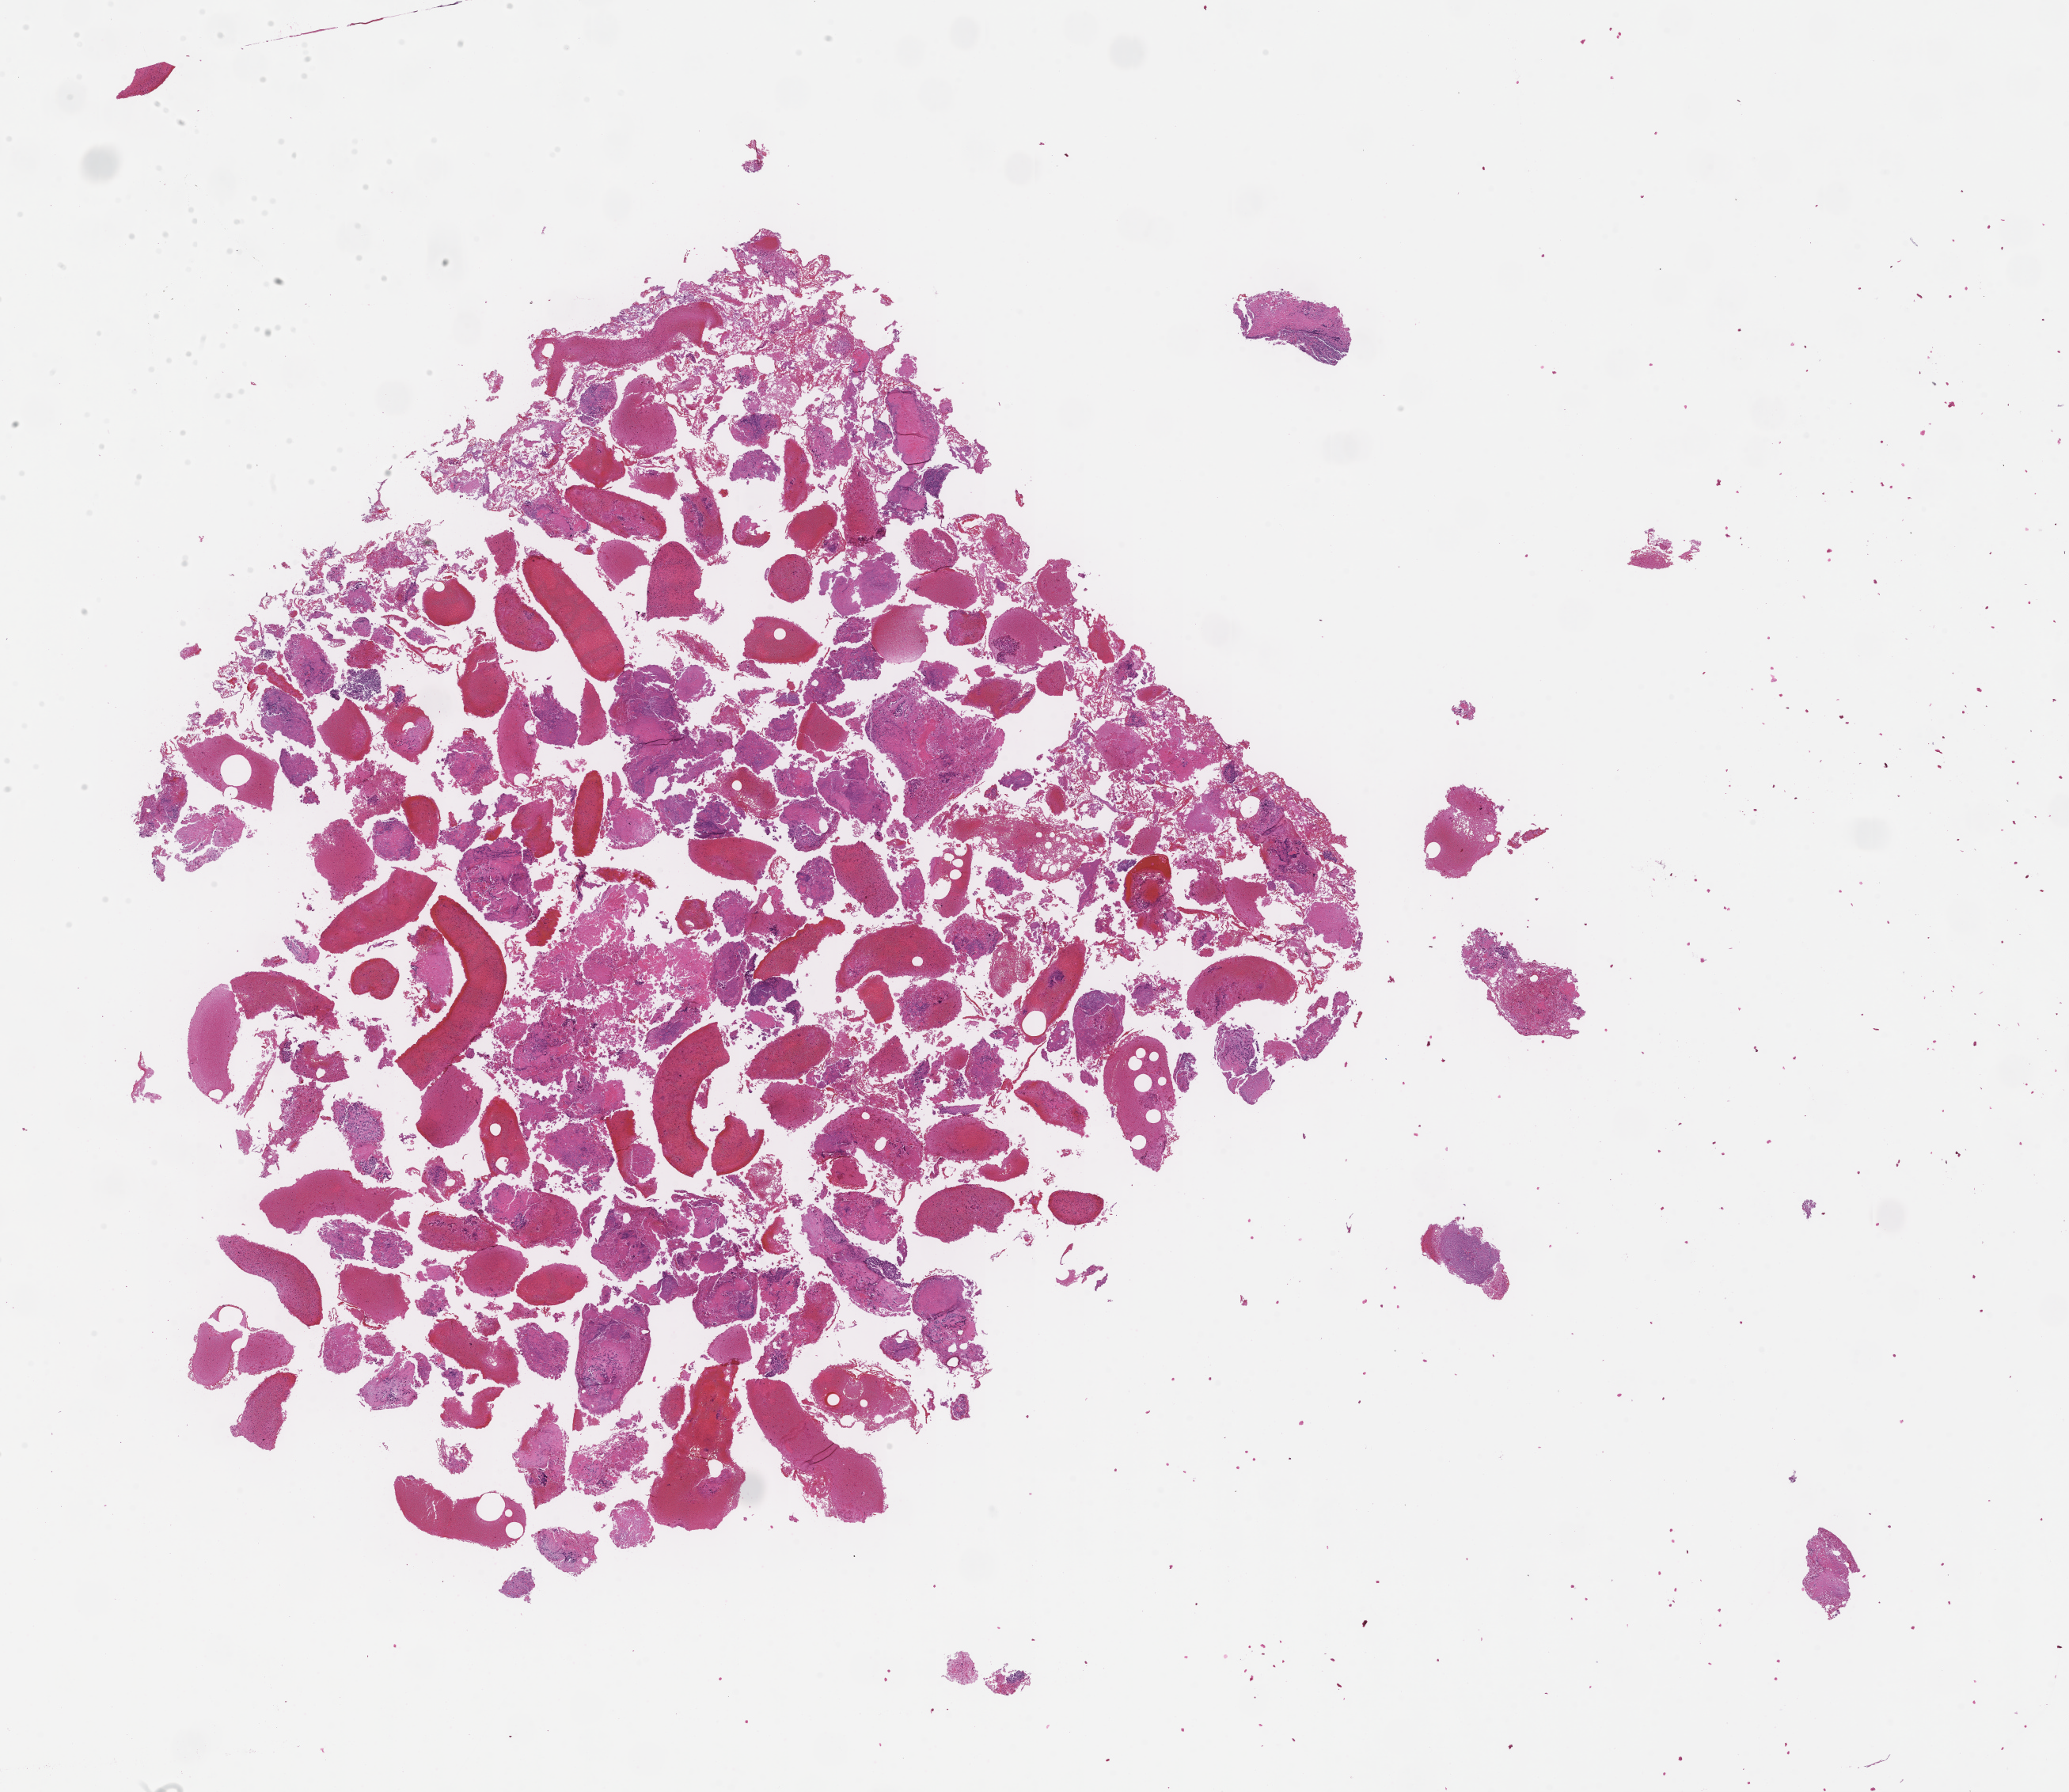
Whole-slide image, hematoxylin and eosin (H&E) stain, shown as a low-resolution overview of the whole scanned area (about 21.1 x 18.3 mm), formalin-fixed paraffin-embedded section, archival tissue. Male patient.
This section: metastasis (sampled organ not recorded). Primary diagnosis of the patient: Small Cell Lung Carcinoma.